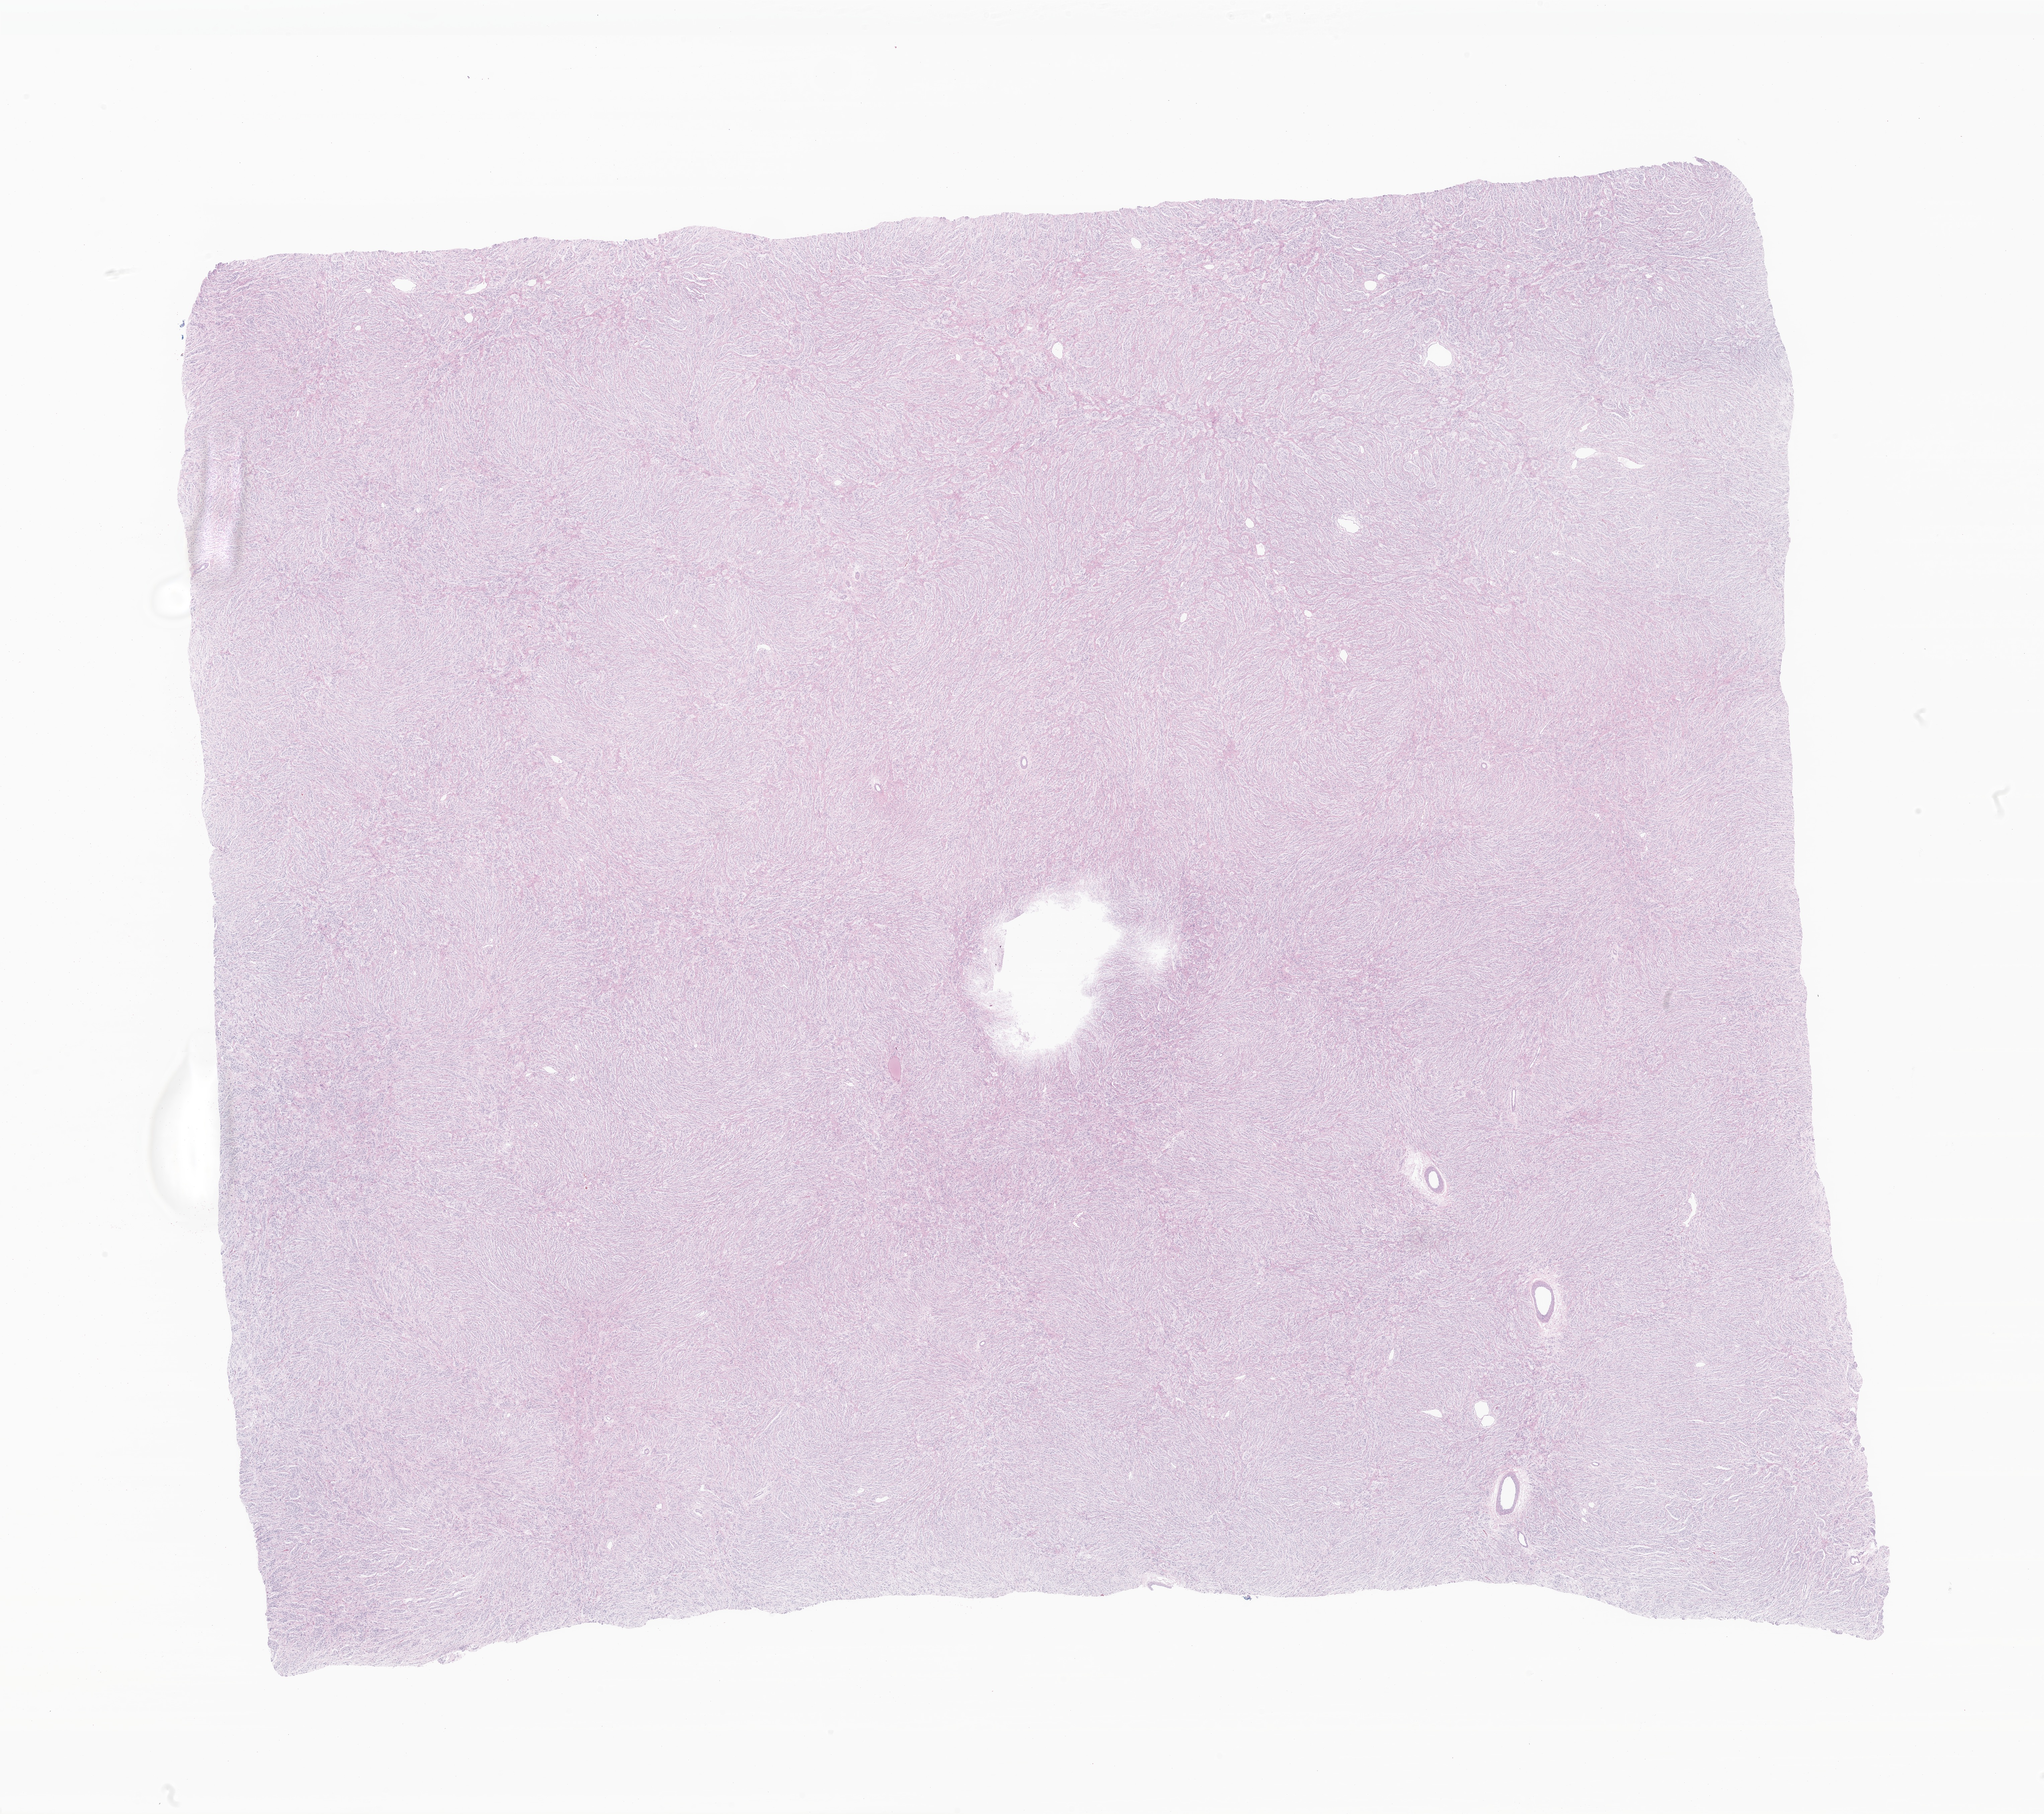
Whole-slide image, haematoxylin and eosin stain of tumor tissue from the brain — a low-resolution overview of the entire scanned area, about 25.8 x 22.9 mm. FFPE section. Patient male; age 208 days.
Recorded diagnosis: Glioma, malignant.